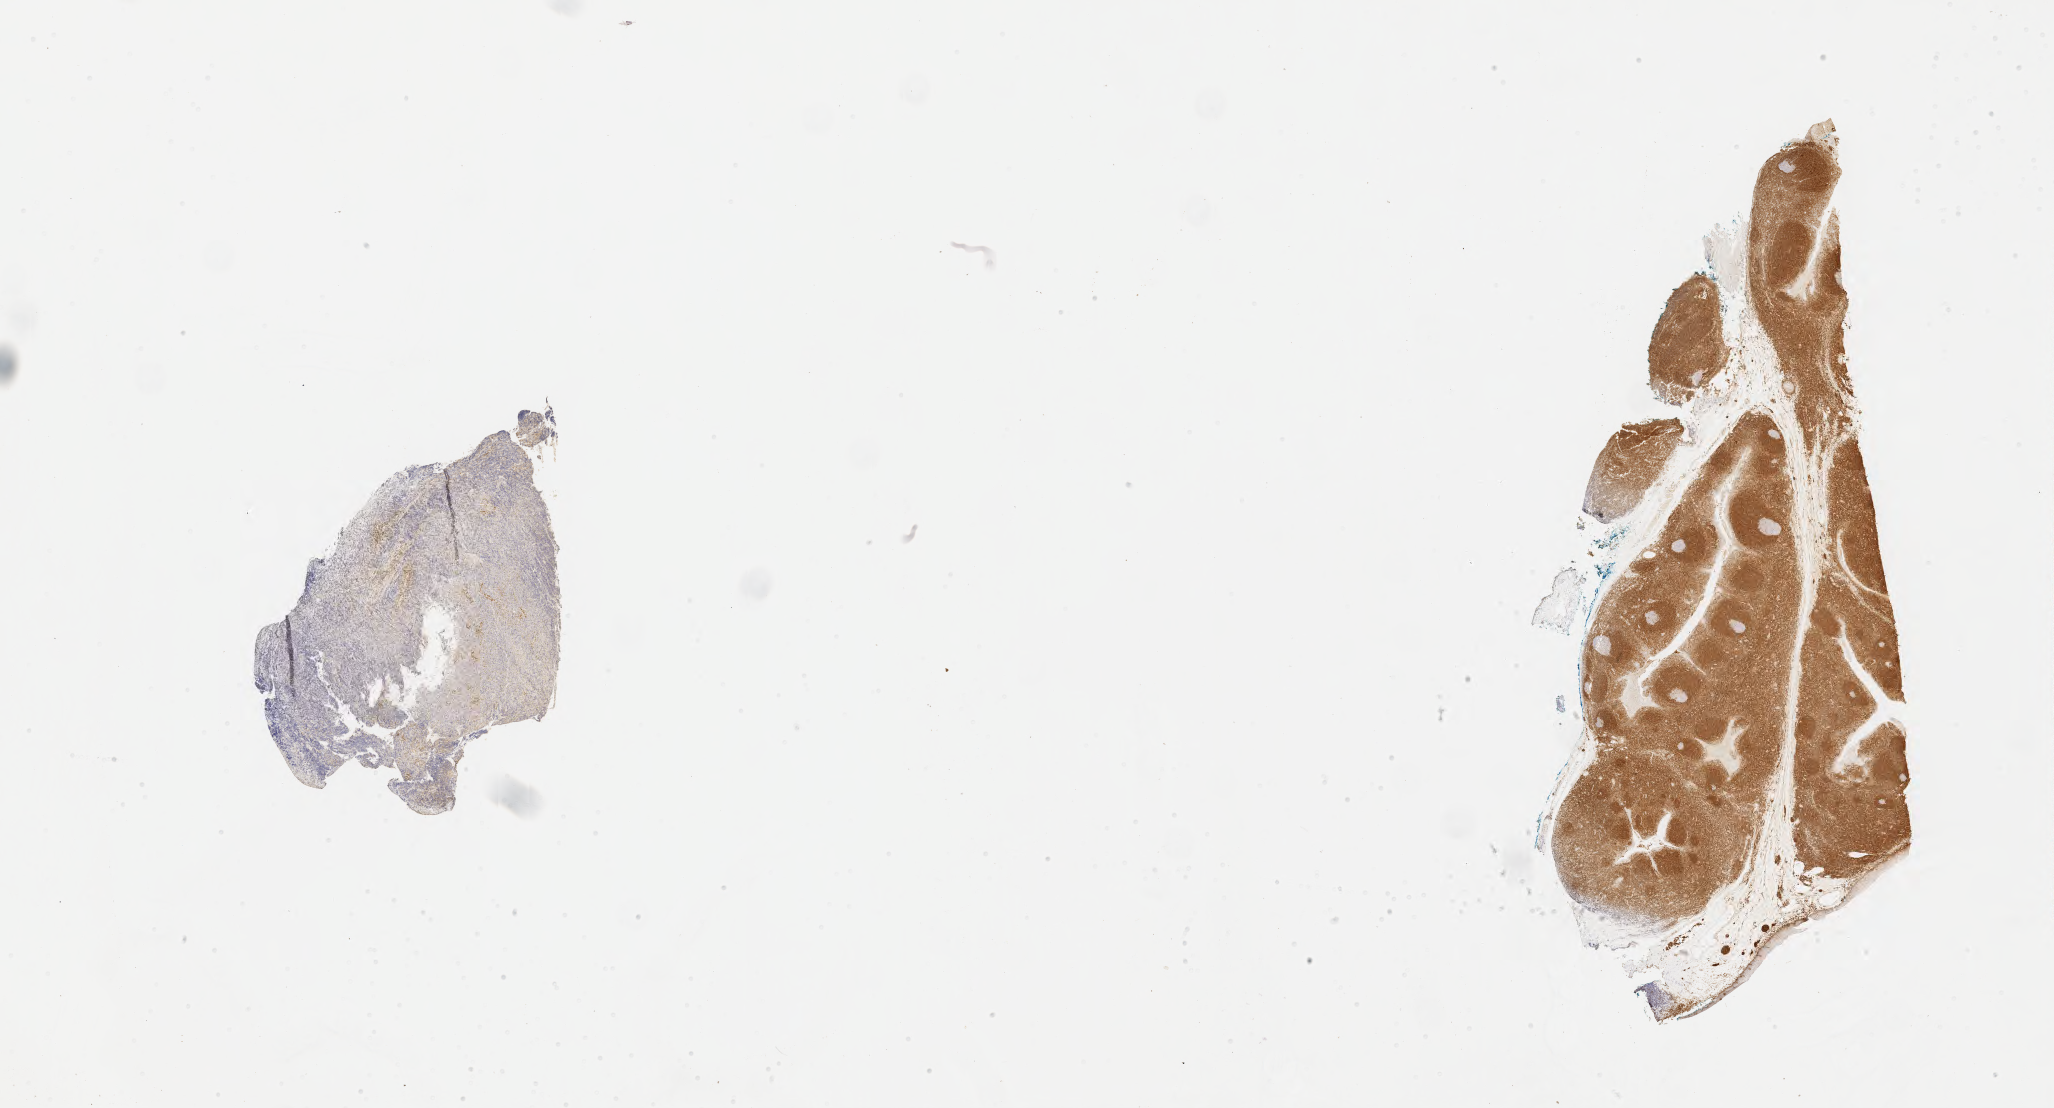
Whole-slide image, immunohistochemical stain for BCL2, whole scanned area (about 33.2 x 17.9 mm) shown as a low-resolution overview. Specimen: tumor tissue. Anatomic site: ovary. Female, age 3 years at initial diagnosis.
Histologic diagnosis: Burkitt lymphoma, NOS.